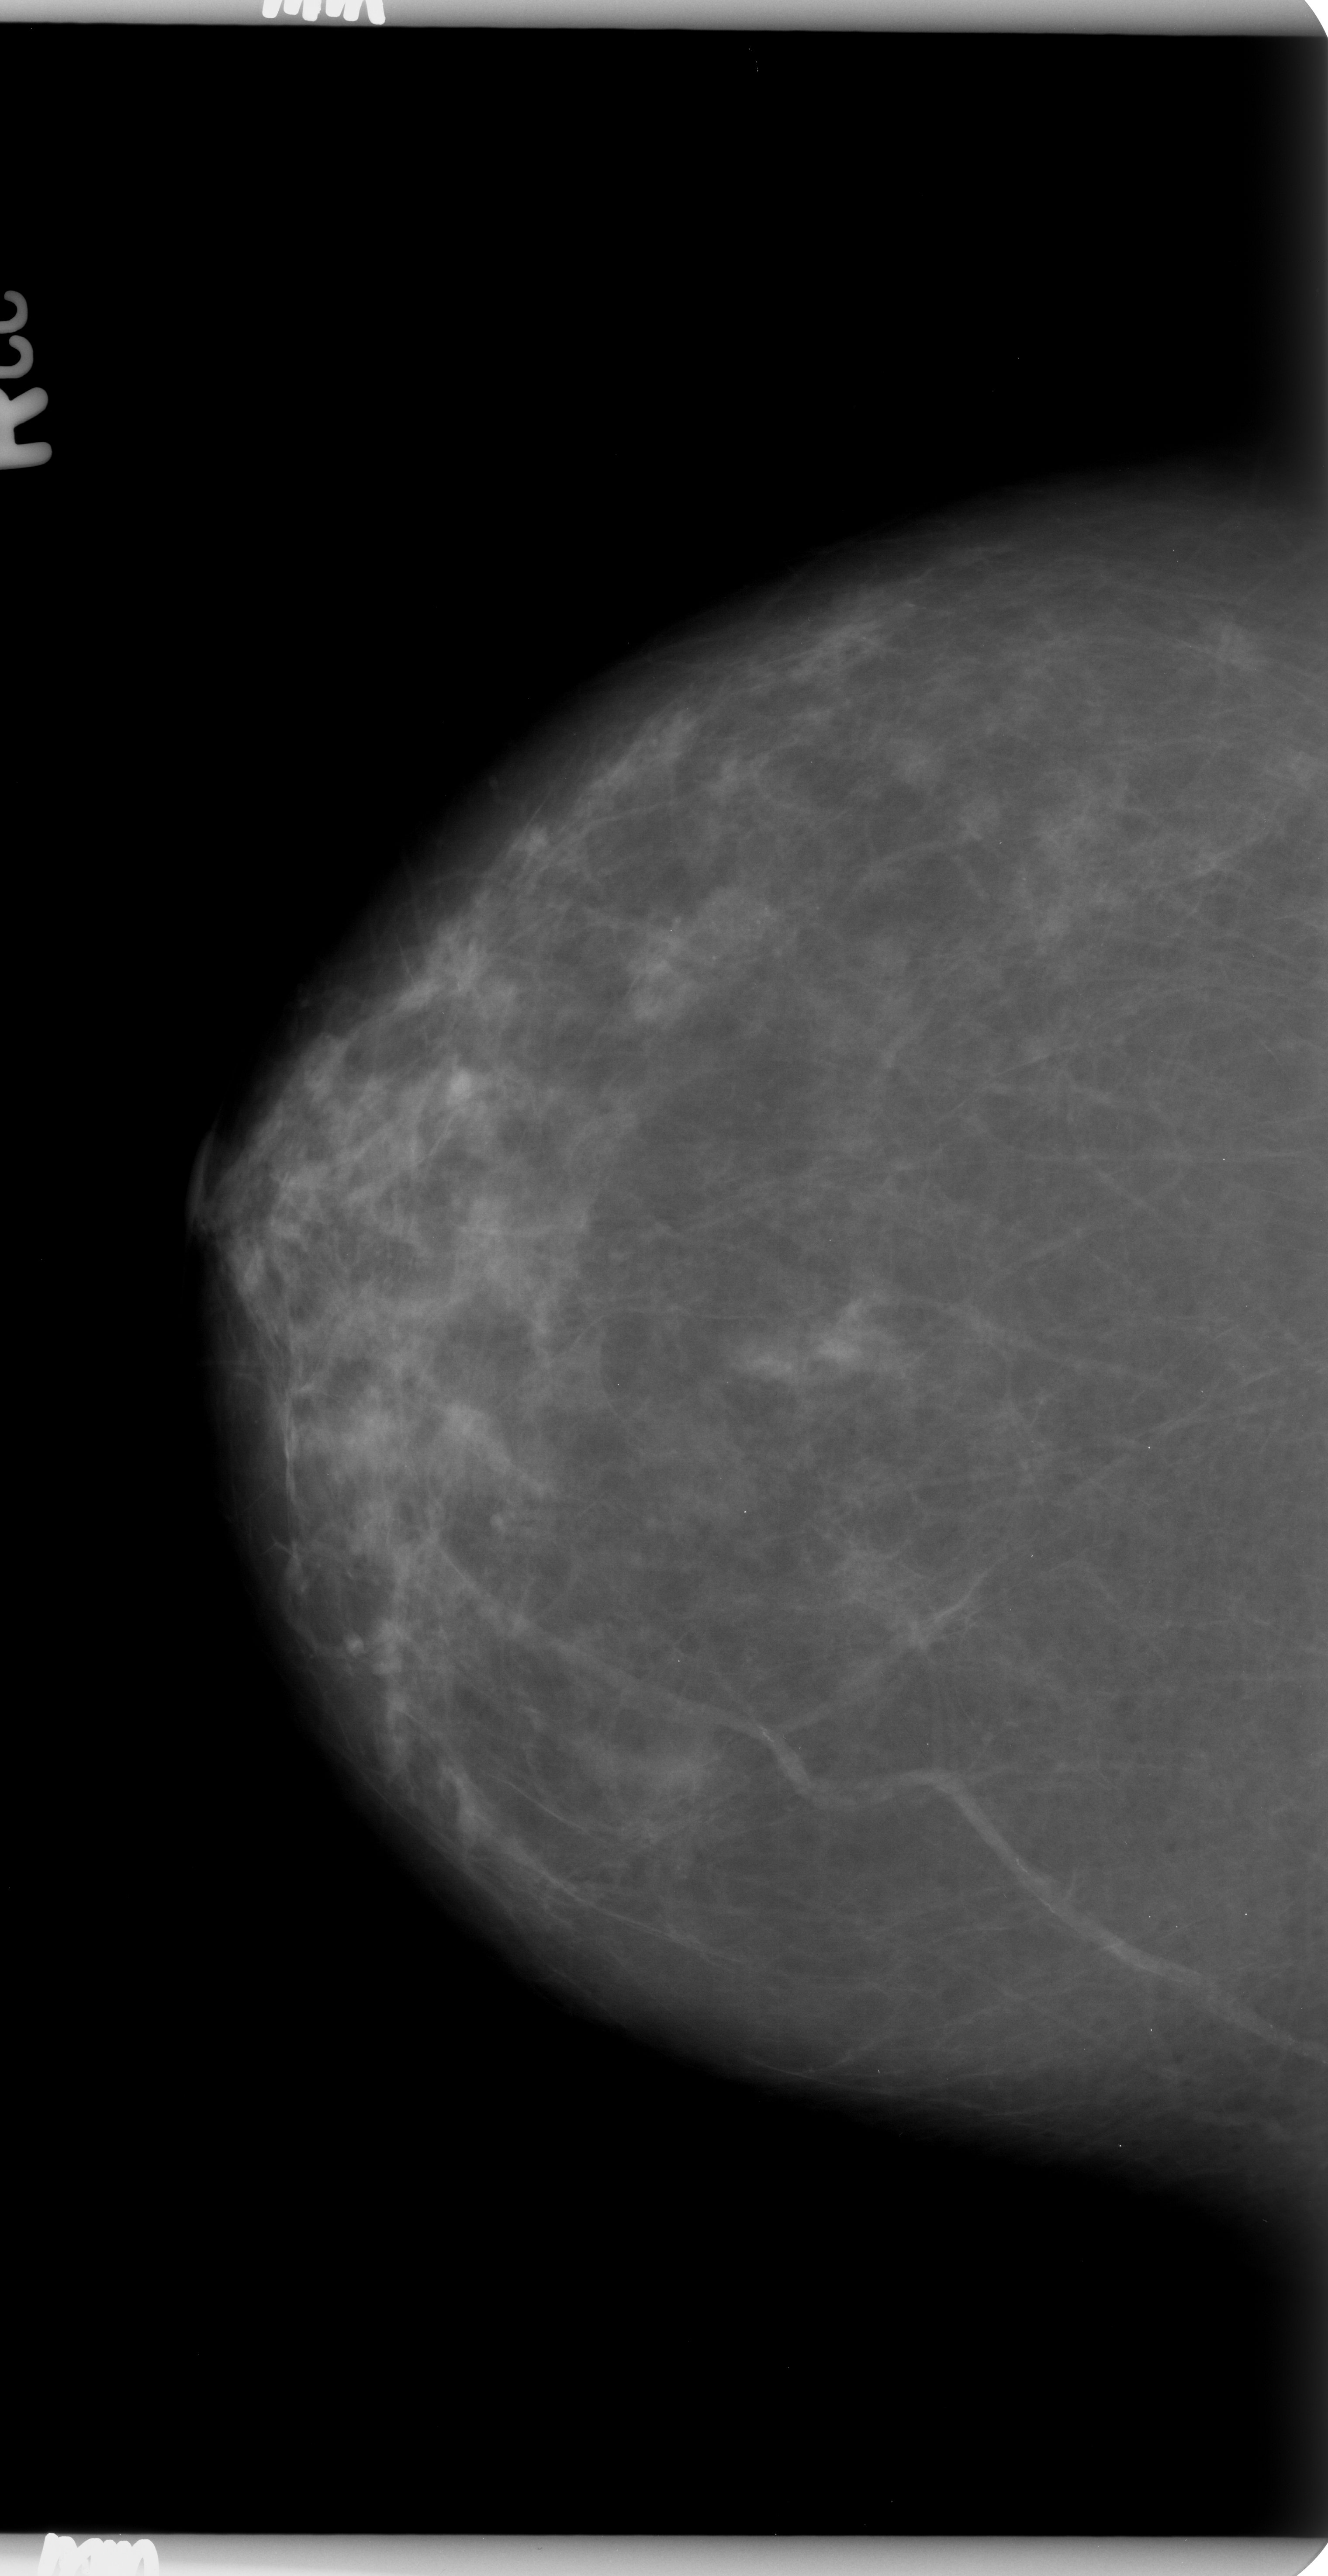
Digitized screen-film mammogram; right breast; craniocaudal (CC) view; 1328 × 2576 image matrix.
Expert-marked regions of interest on this image (one box per marked abnormality):
- calcifications, morphology round and regular, distribution clustered; BI-RADS assessment category 3; subtlety rating 3 on a 1 (subtle) to 5 (obvious) scale; pathology result (as recorded, not read from the image): benign: bounding box [x1, y1, x2, y2] px = [684, 866, 794, 980]